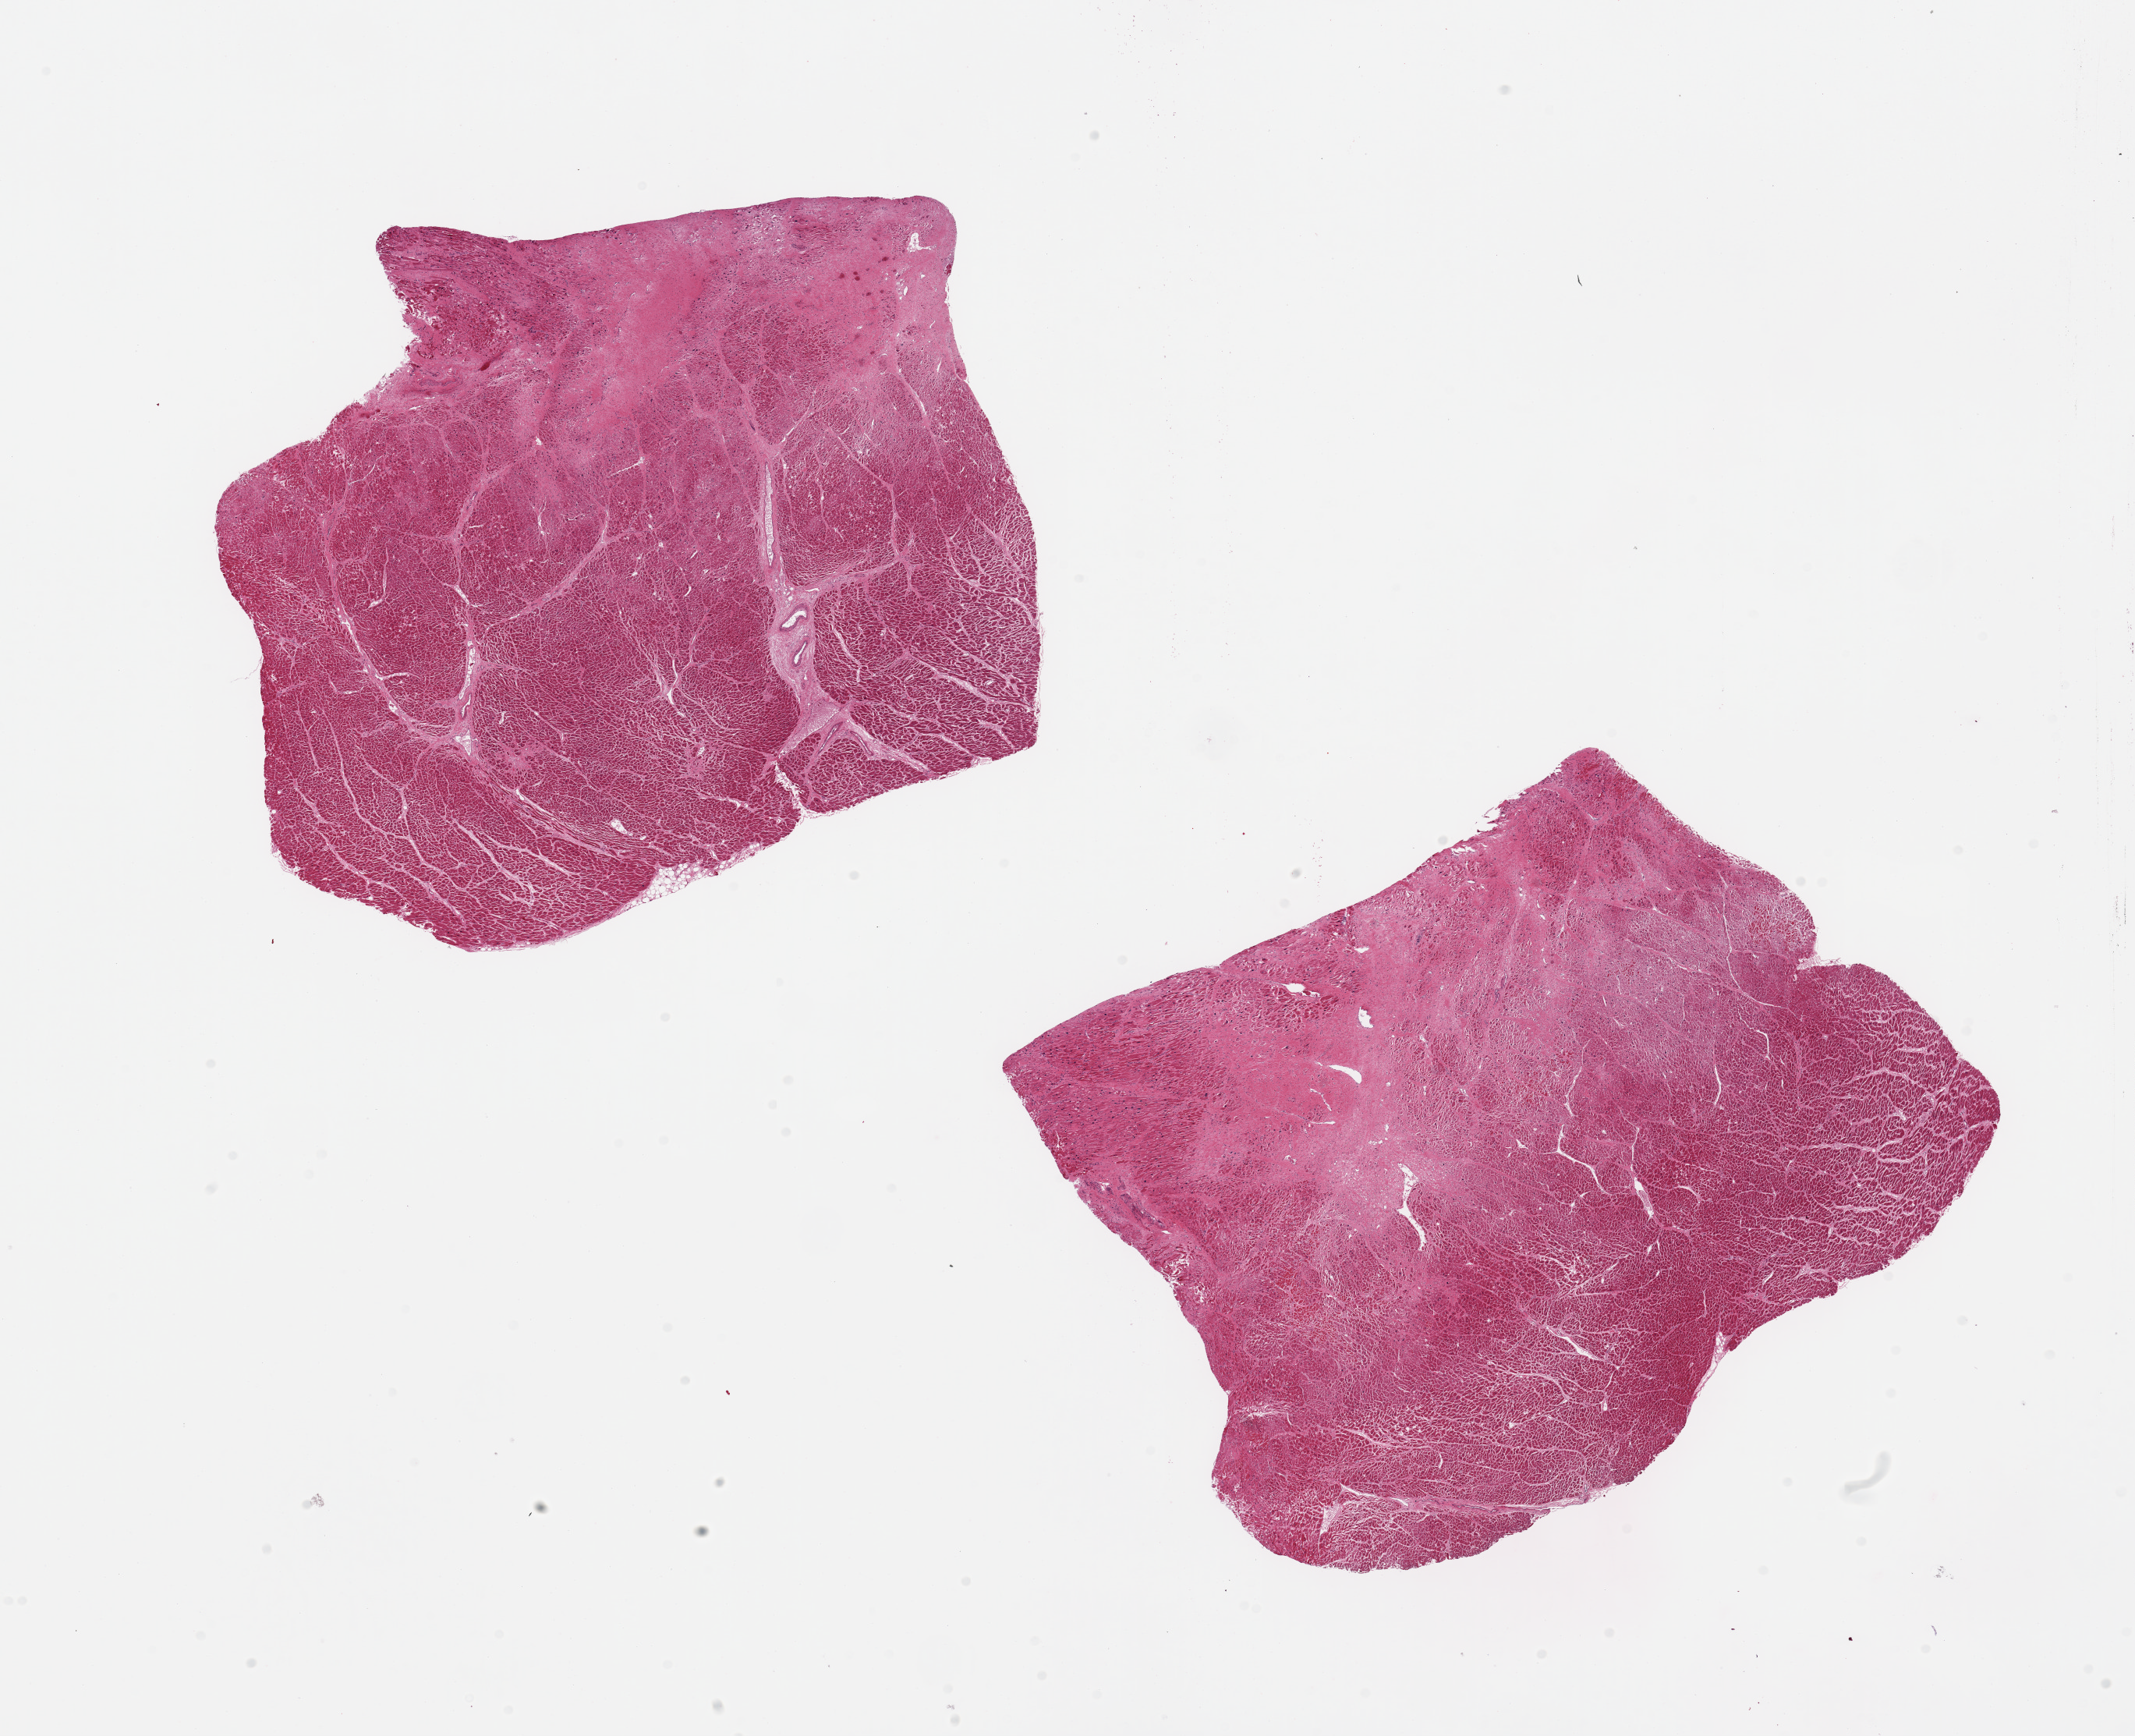
Hematoxylin and eosin (H&E) whole-slide image, a low-resolution overview of the entire scanned area, about 21.7 x 17.6 mm (from a 20x scan), PAXgene-fixed paraffin-embedded (PFPE) section, section of heart (target tissue), donor tissue sample.
Review note (as recorded): 2 pieces, subacute/remote infarct.